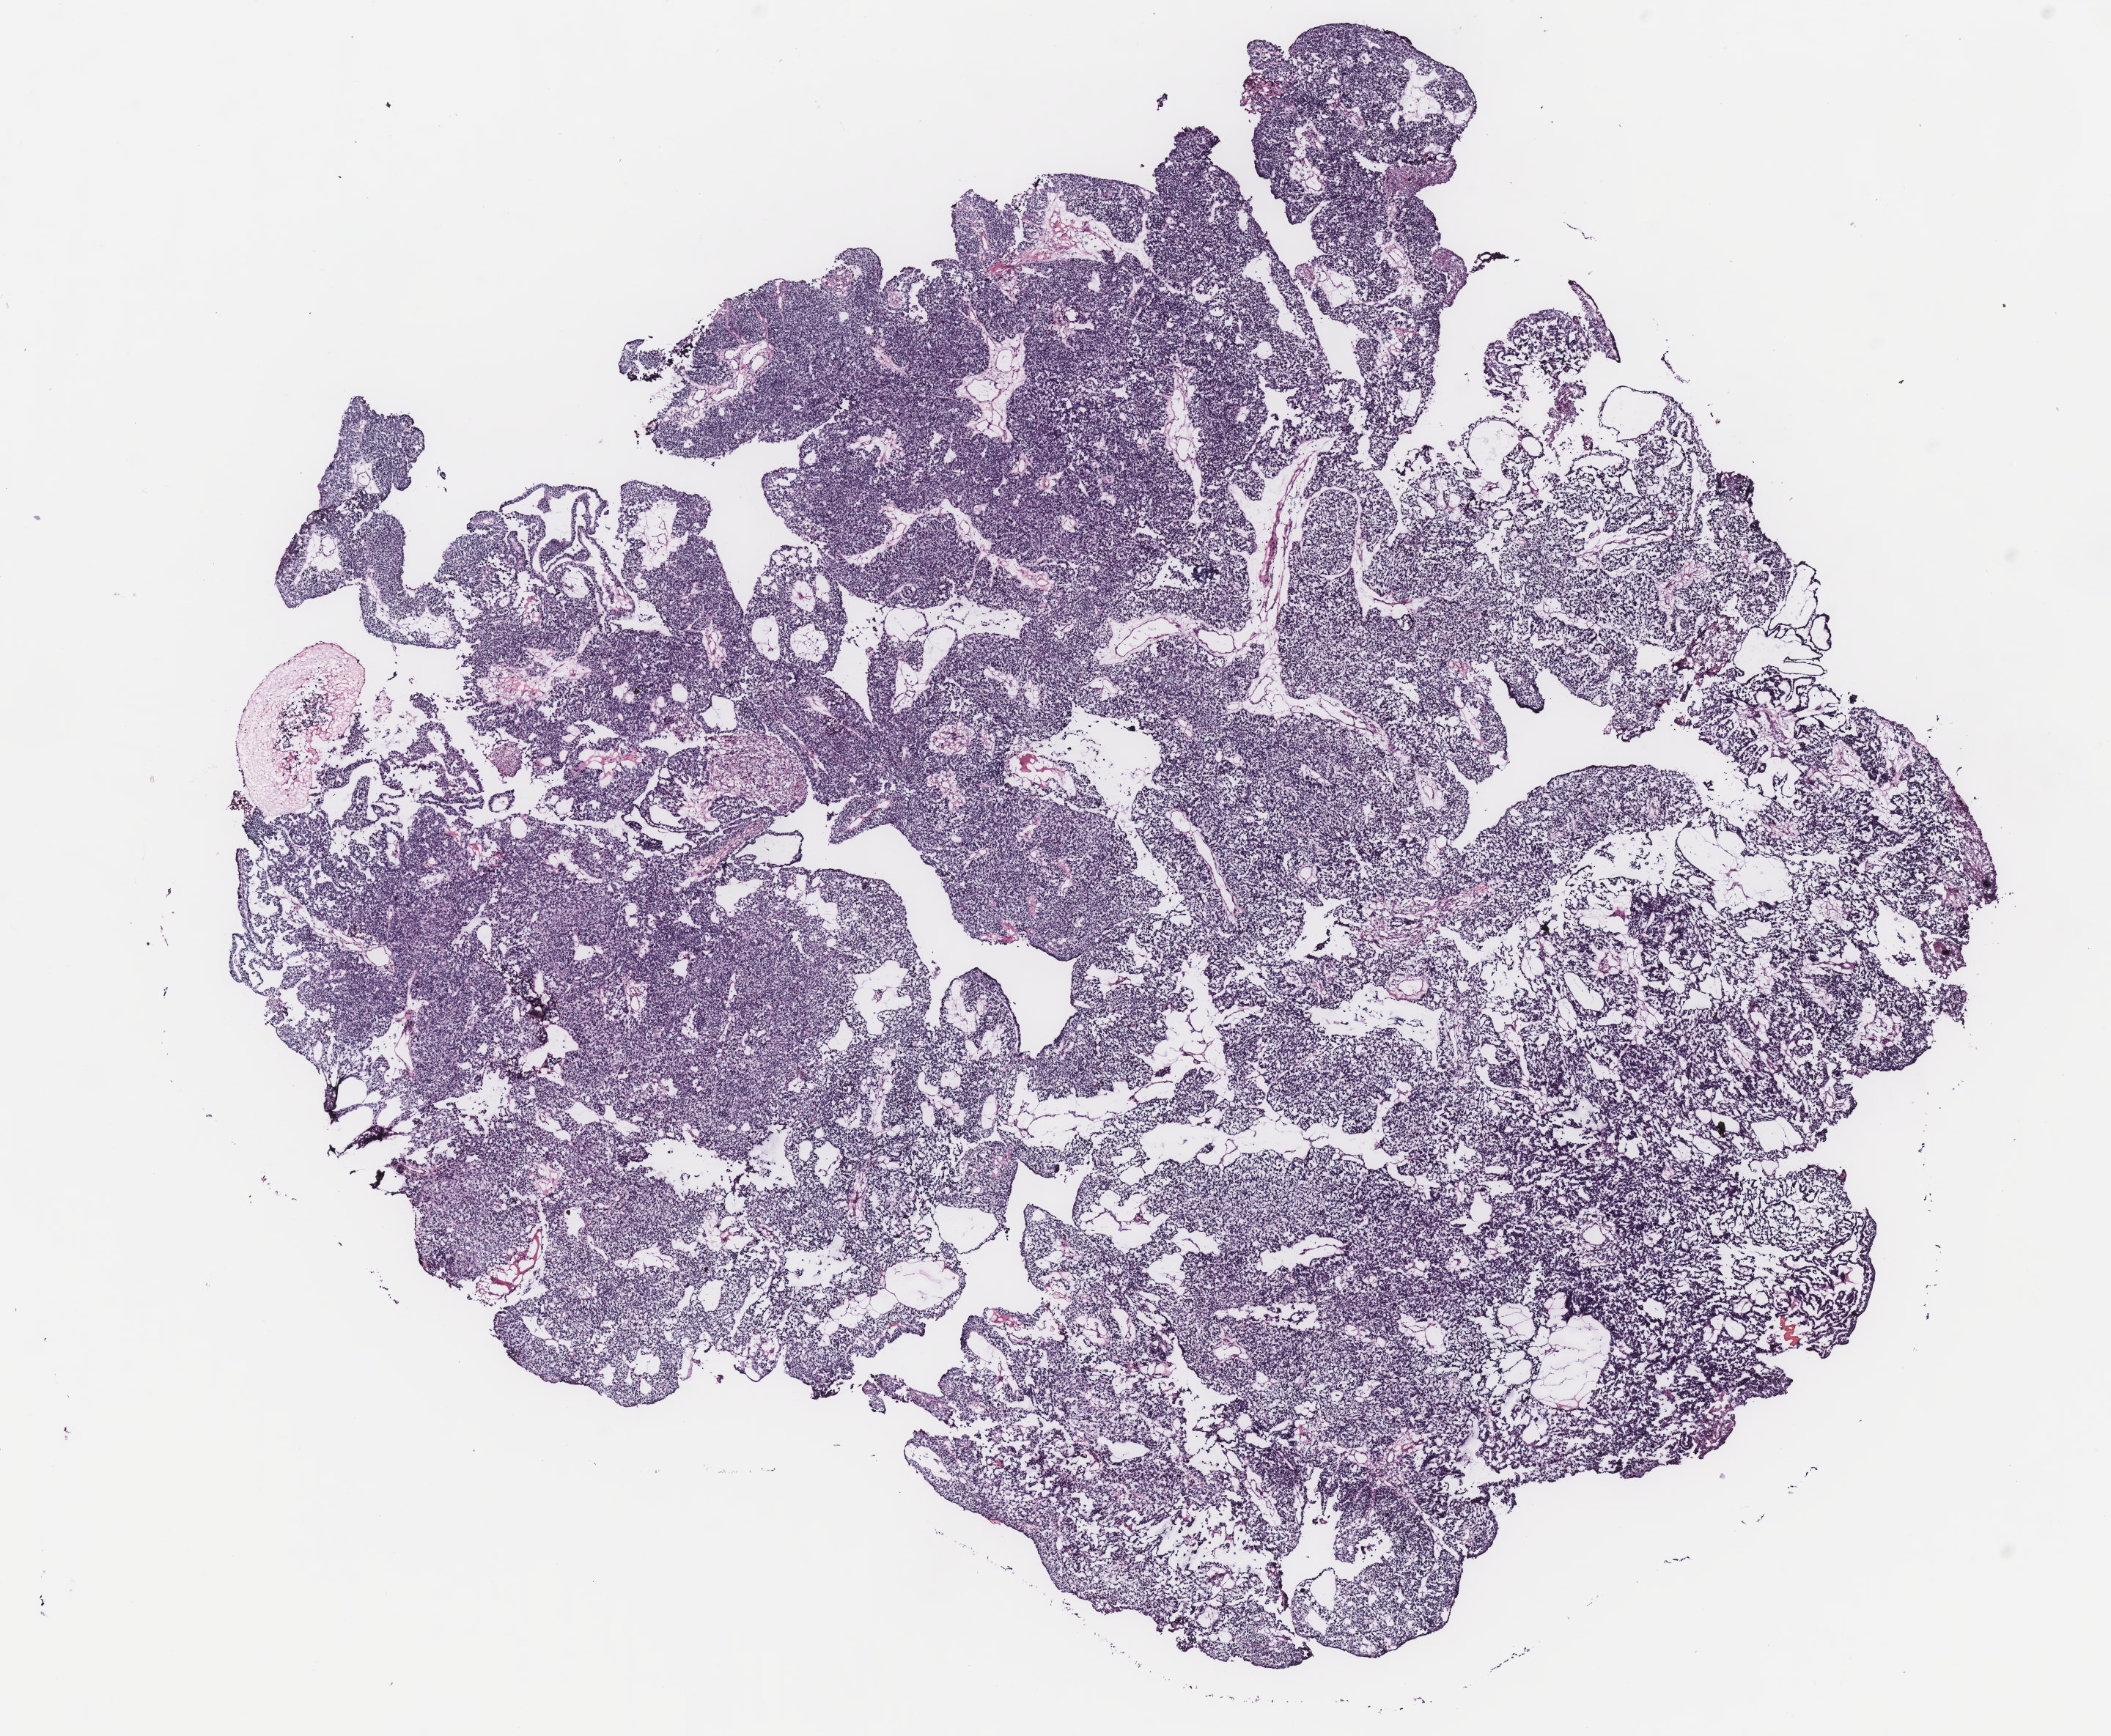
H&E whole-slide image — a low-resolution overview of the entire scanned area, about 11.5 x 9.5 mm (acquisition: 40x scan); ovary, tissue type not recorded.
Patient diagnosis (cohort enrolment): ovarian cancer (ovary).